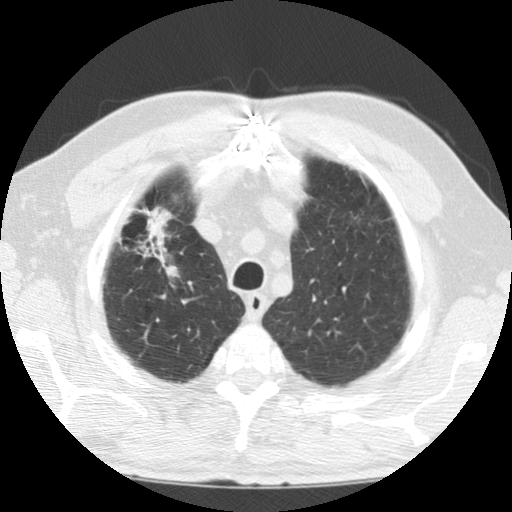
Chest CT (low-dose screening protocol), one axial image, baseline screening round, lung window (W 1500 / L -600 HU), 2.5 mm slice thickness, 120 kVp, slice 18 of 124 in the series. Male, age 69 years at enrolment. Former smoker at enrolment.
- Lesion marked by an expert reader, box from (x=104, y=211) to (x=192, y=293) px.
- Screening reader's record for this exam: no non-calcified nodule ≥4 mm recorded.
- Later outcome: lung cancer diagnosed 171 days after this screen — adenocarcinoma, NOS, right upper lobe, poorly differentiated (G3), stage IIIB (AJCC 6th edition), 40 mm at pathology.